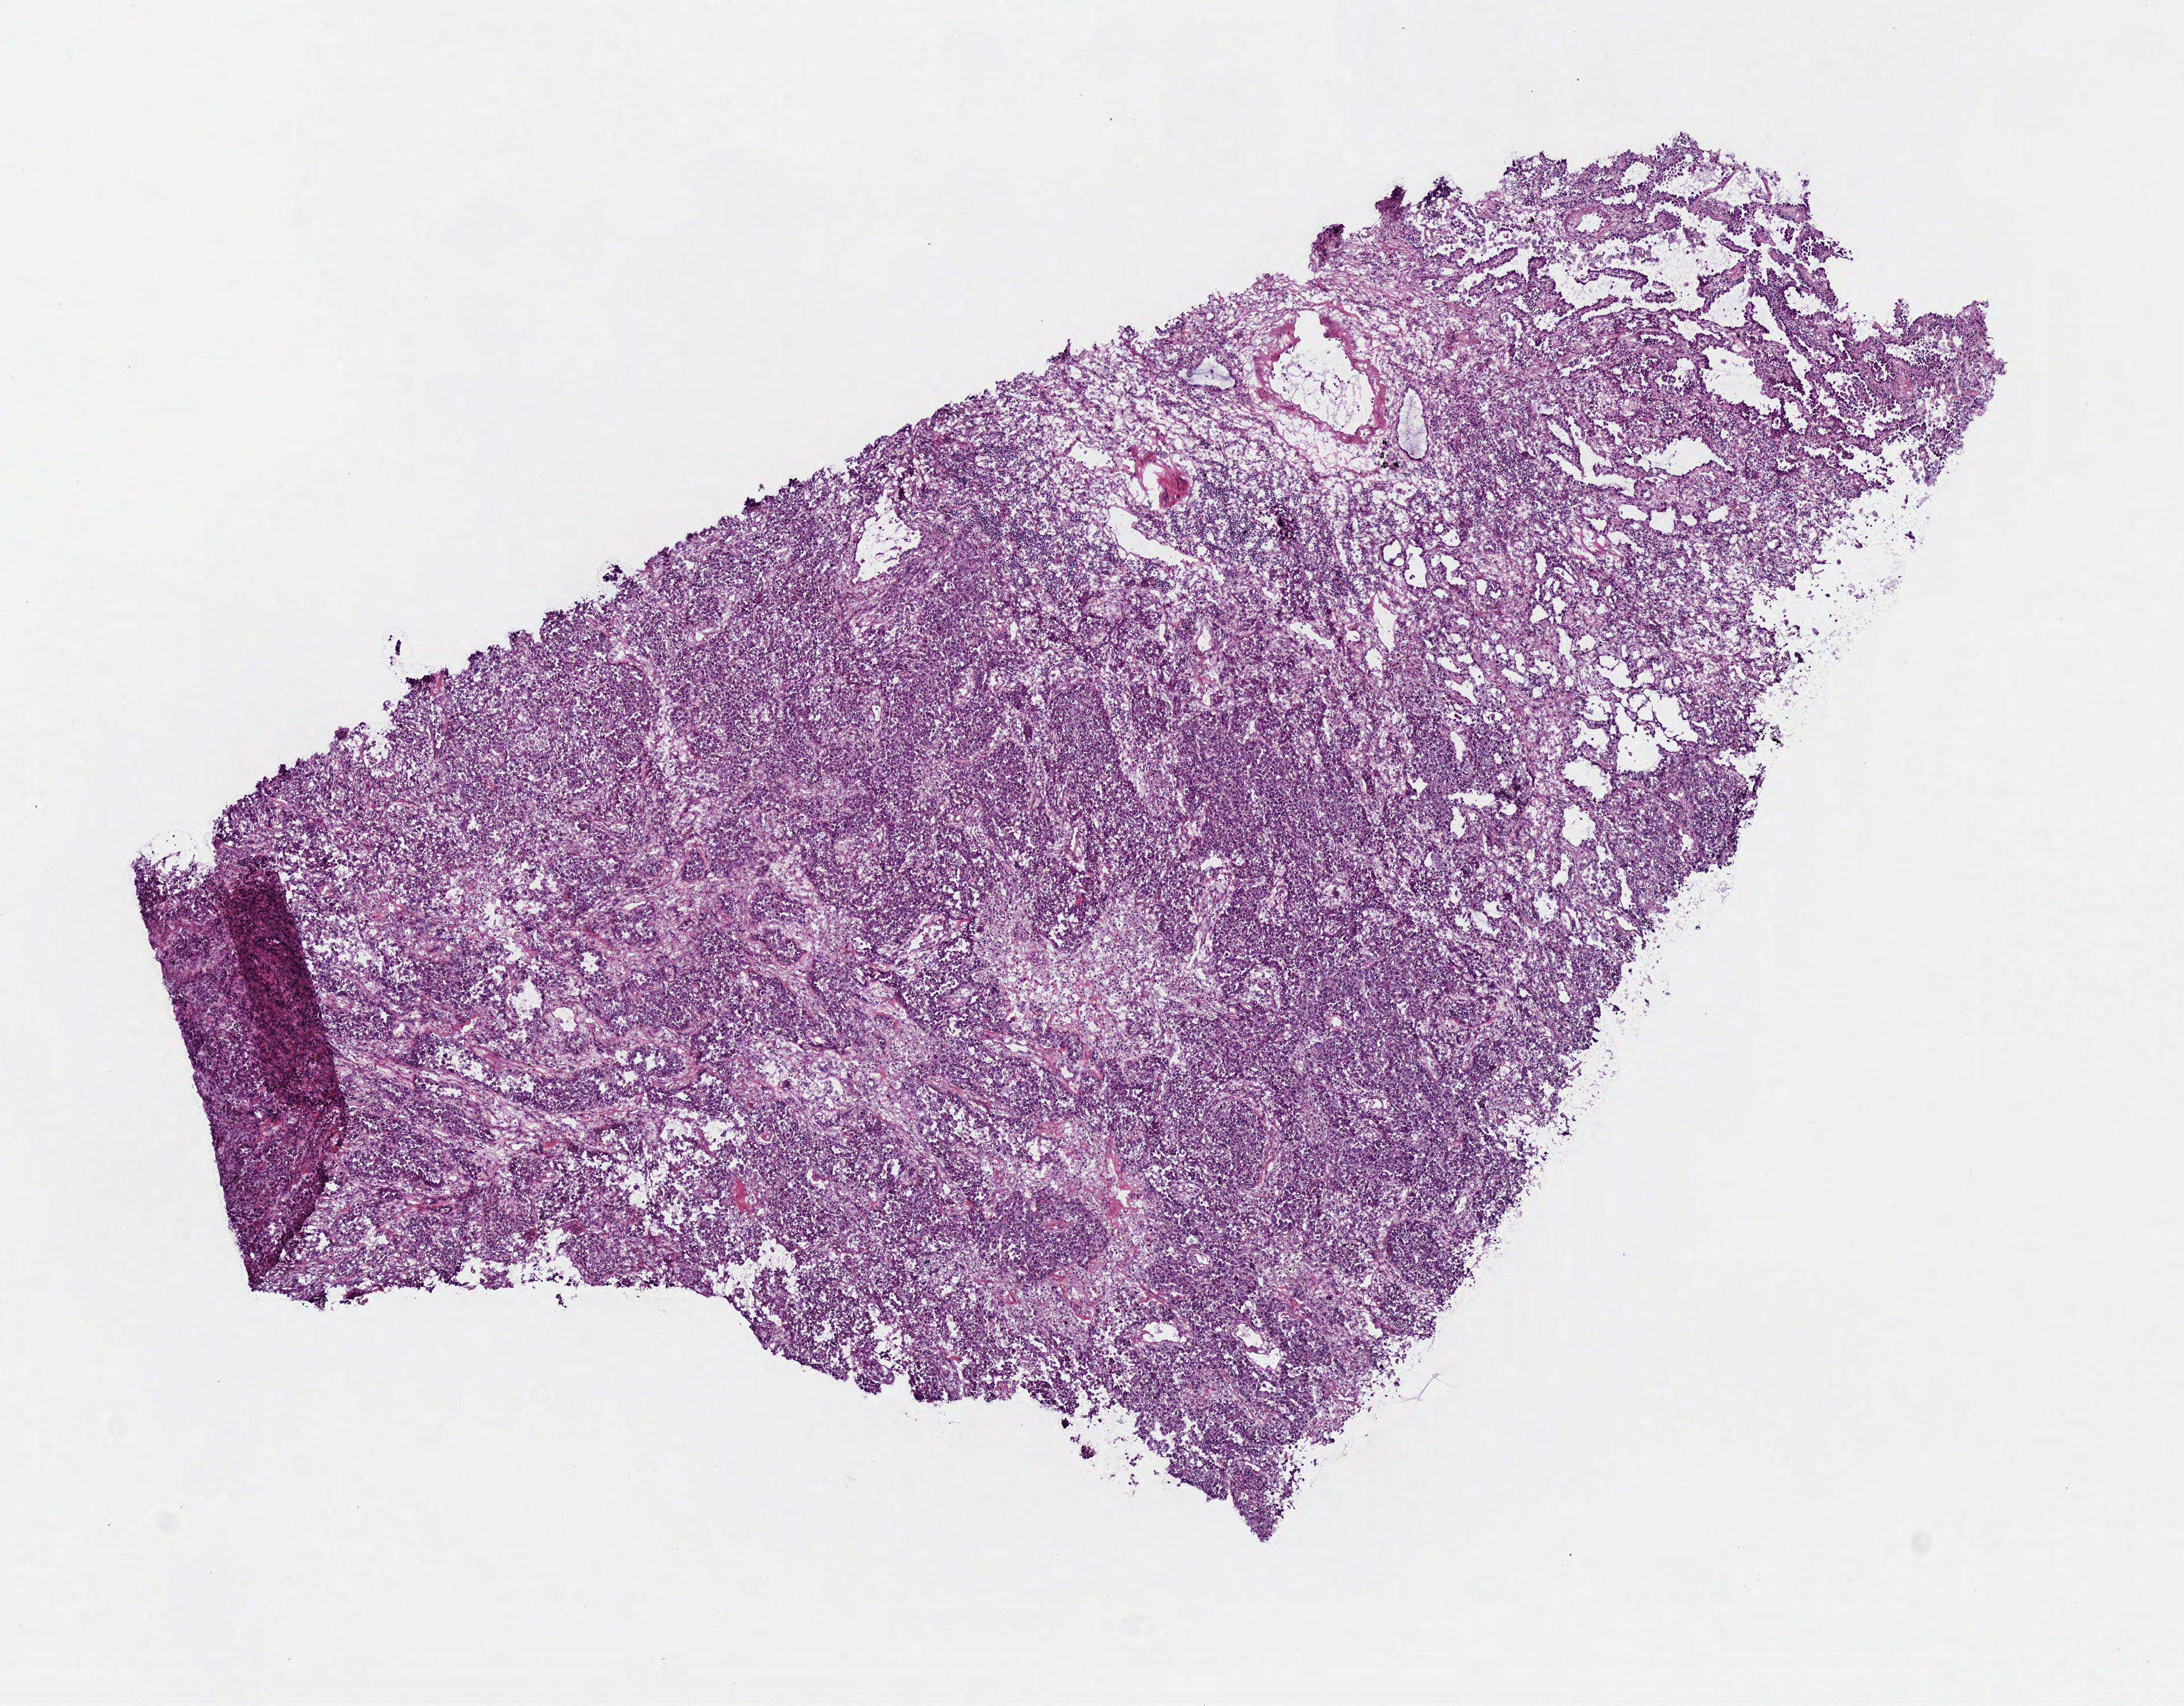
Whole-slide histology image, H&E-stained, whole scanned area (about 7.5 x 5.9 mm, from a 40x scan) shown as a low-resolution overview. Frozen section. Sample: primary tumour, lung. Patient sex: male. Composition of this section per pathologist review: tumour cells 85%, tumour nuclei 80%, normal cells 15%, stromal cells 0%, necrosis 0%. Infiltration values recorded for this section: lymphocyte infiltration 10%, monocyte infiltration 2%, neutrophil infiltration 0%.
Pathologic diagnosis: Adenocarcinoma, NOS. AJCC pathologic stage: IIIA (6th edition). Laterality: right.